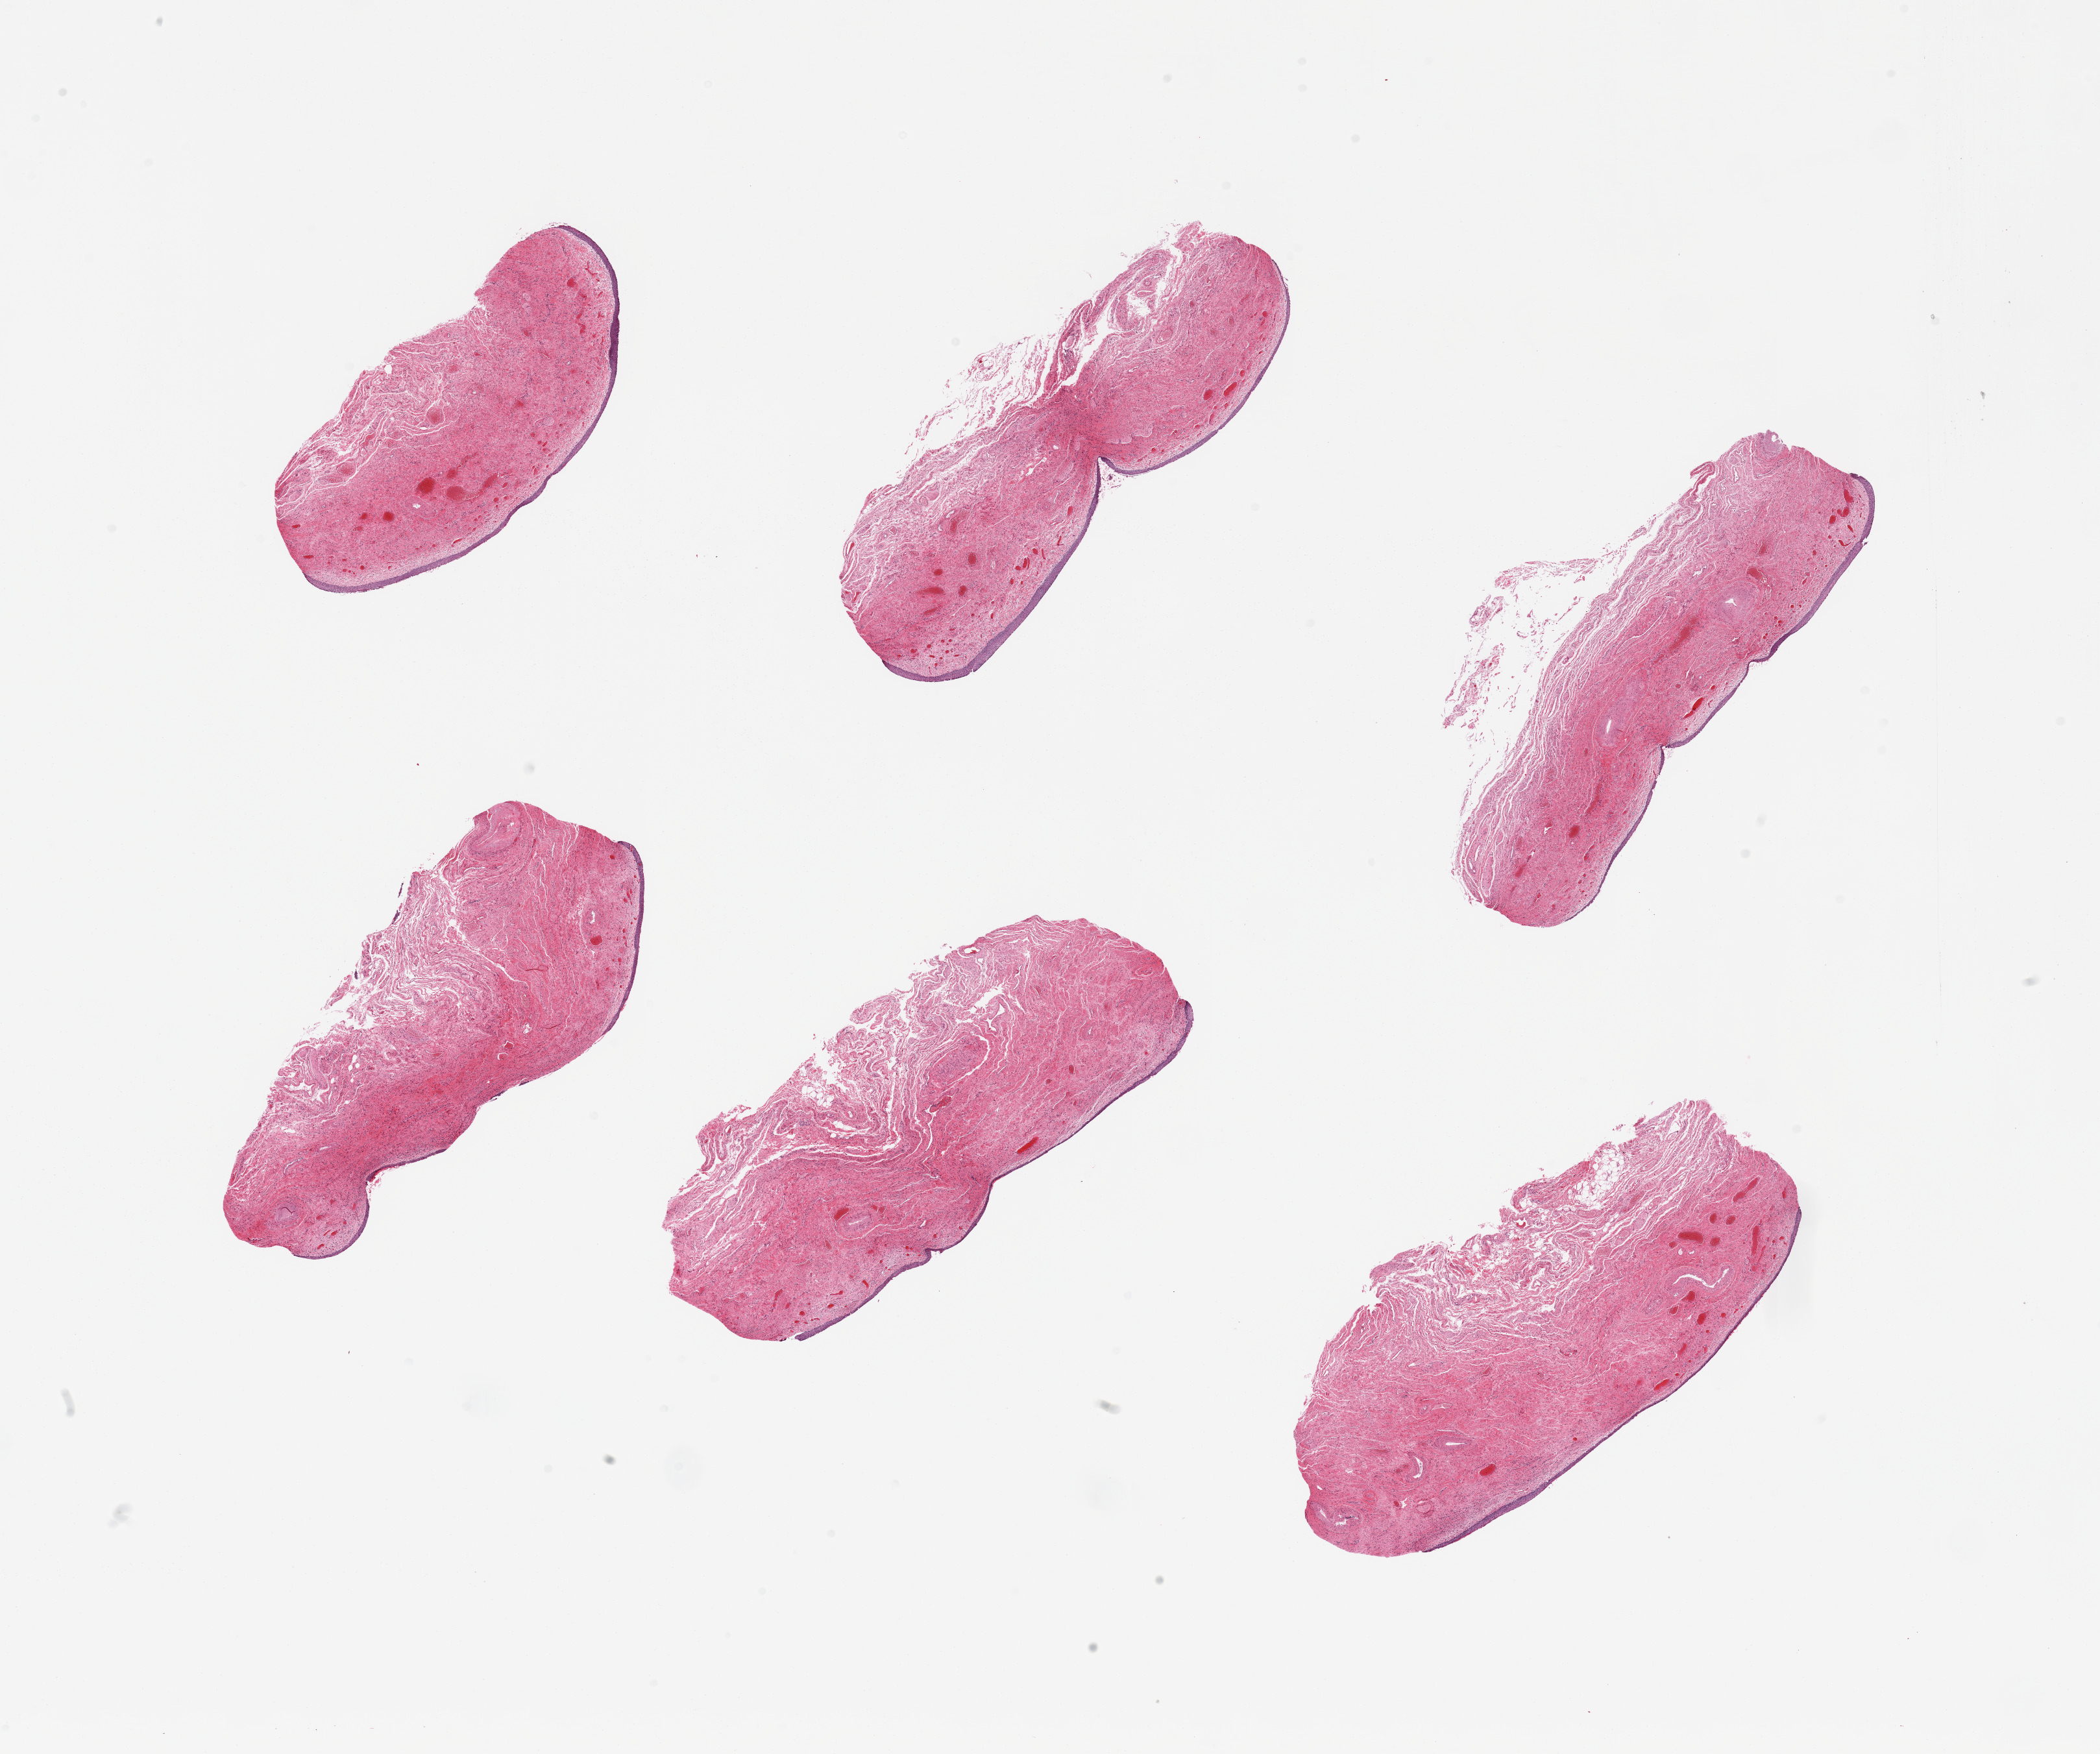
Digitized H&E-stained section — a low-resolution overview of the entire scanned area, about 25.6 x 21.4 mm; PAXgene-fixed paraffin-embedded (PFPE) section; sampled site (target tissue): vagina; tissue donor sample. Donor: female.
Pathologist's review note for this sample: 6 pieces; epitheliall desquamation; stroma.